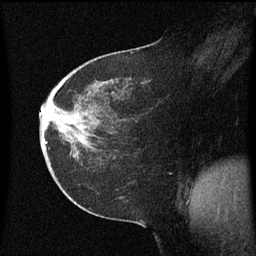
Breast MRI (dynamic contrast-enhanced), one sagittal slice; position 27 of 60 along the scan axis; dynamic contrast-enhanced series, image 2 of 3 at this slice position (ordered by acquisition); 1.5 T; TE 4.2 ms, TR 8.4 ms; 2 mm slice thickness; 256 × 256 image matrix, field of view 200 × 200 mm. Patient: female, 38 years. Case-level facts recorded for this patient, not image findings: setting: breast cancer imaged before/during neoadjuvant chemotherapy; receptor status: HER2-positive.
Annotated regions visible in this slice (semi-automatic segmentation, software-assisted and operator-edited):
- analysis volume of interest (the breast-tissue region the enhancement analysis was run in; not a lesion): bounding box [x1, y1, x2, y2] px = [40, 50, 148, 185]
- tumour enhancement mask (voxels above the 70 % enhancement threshold inside the analysis volume of interest): [41, 112, 77, 157]